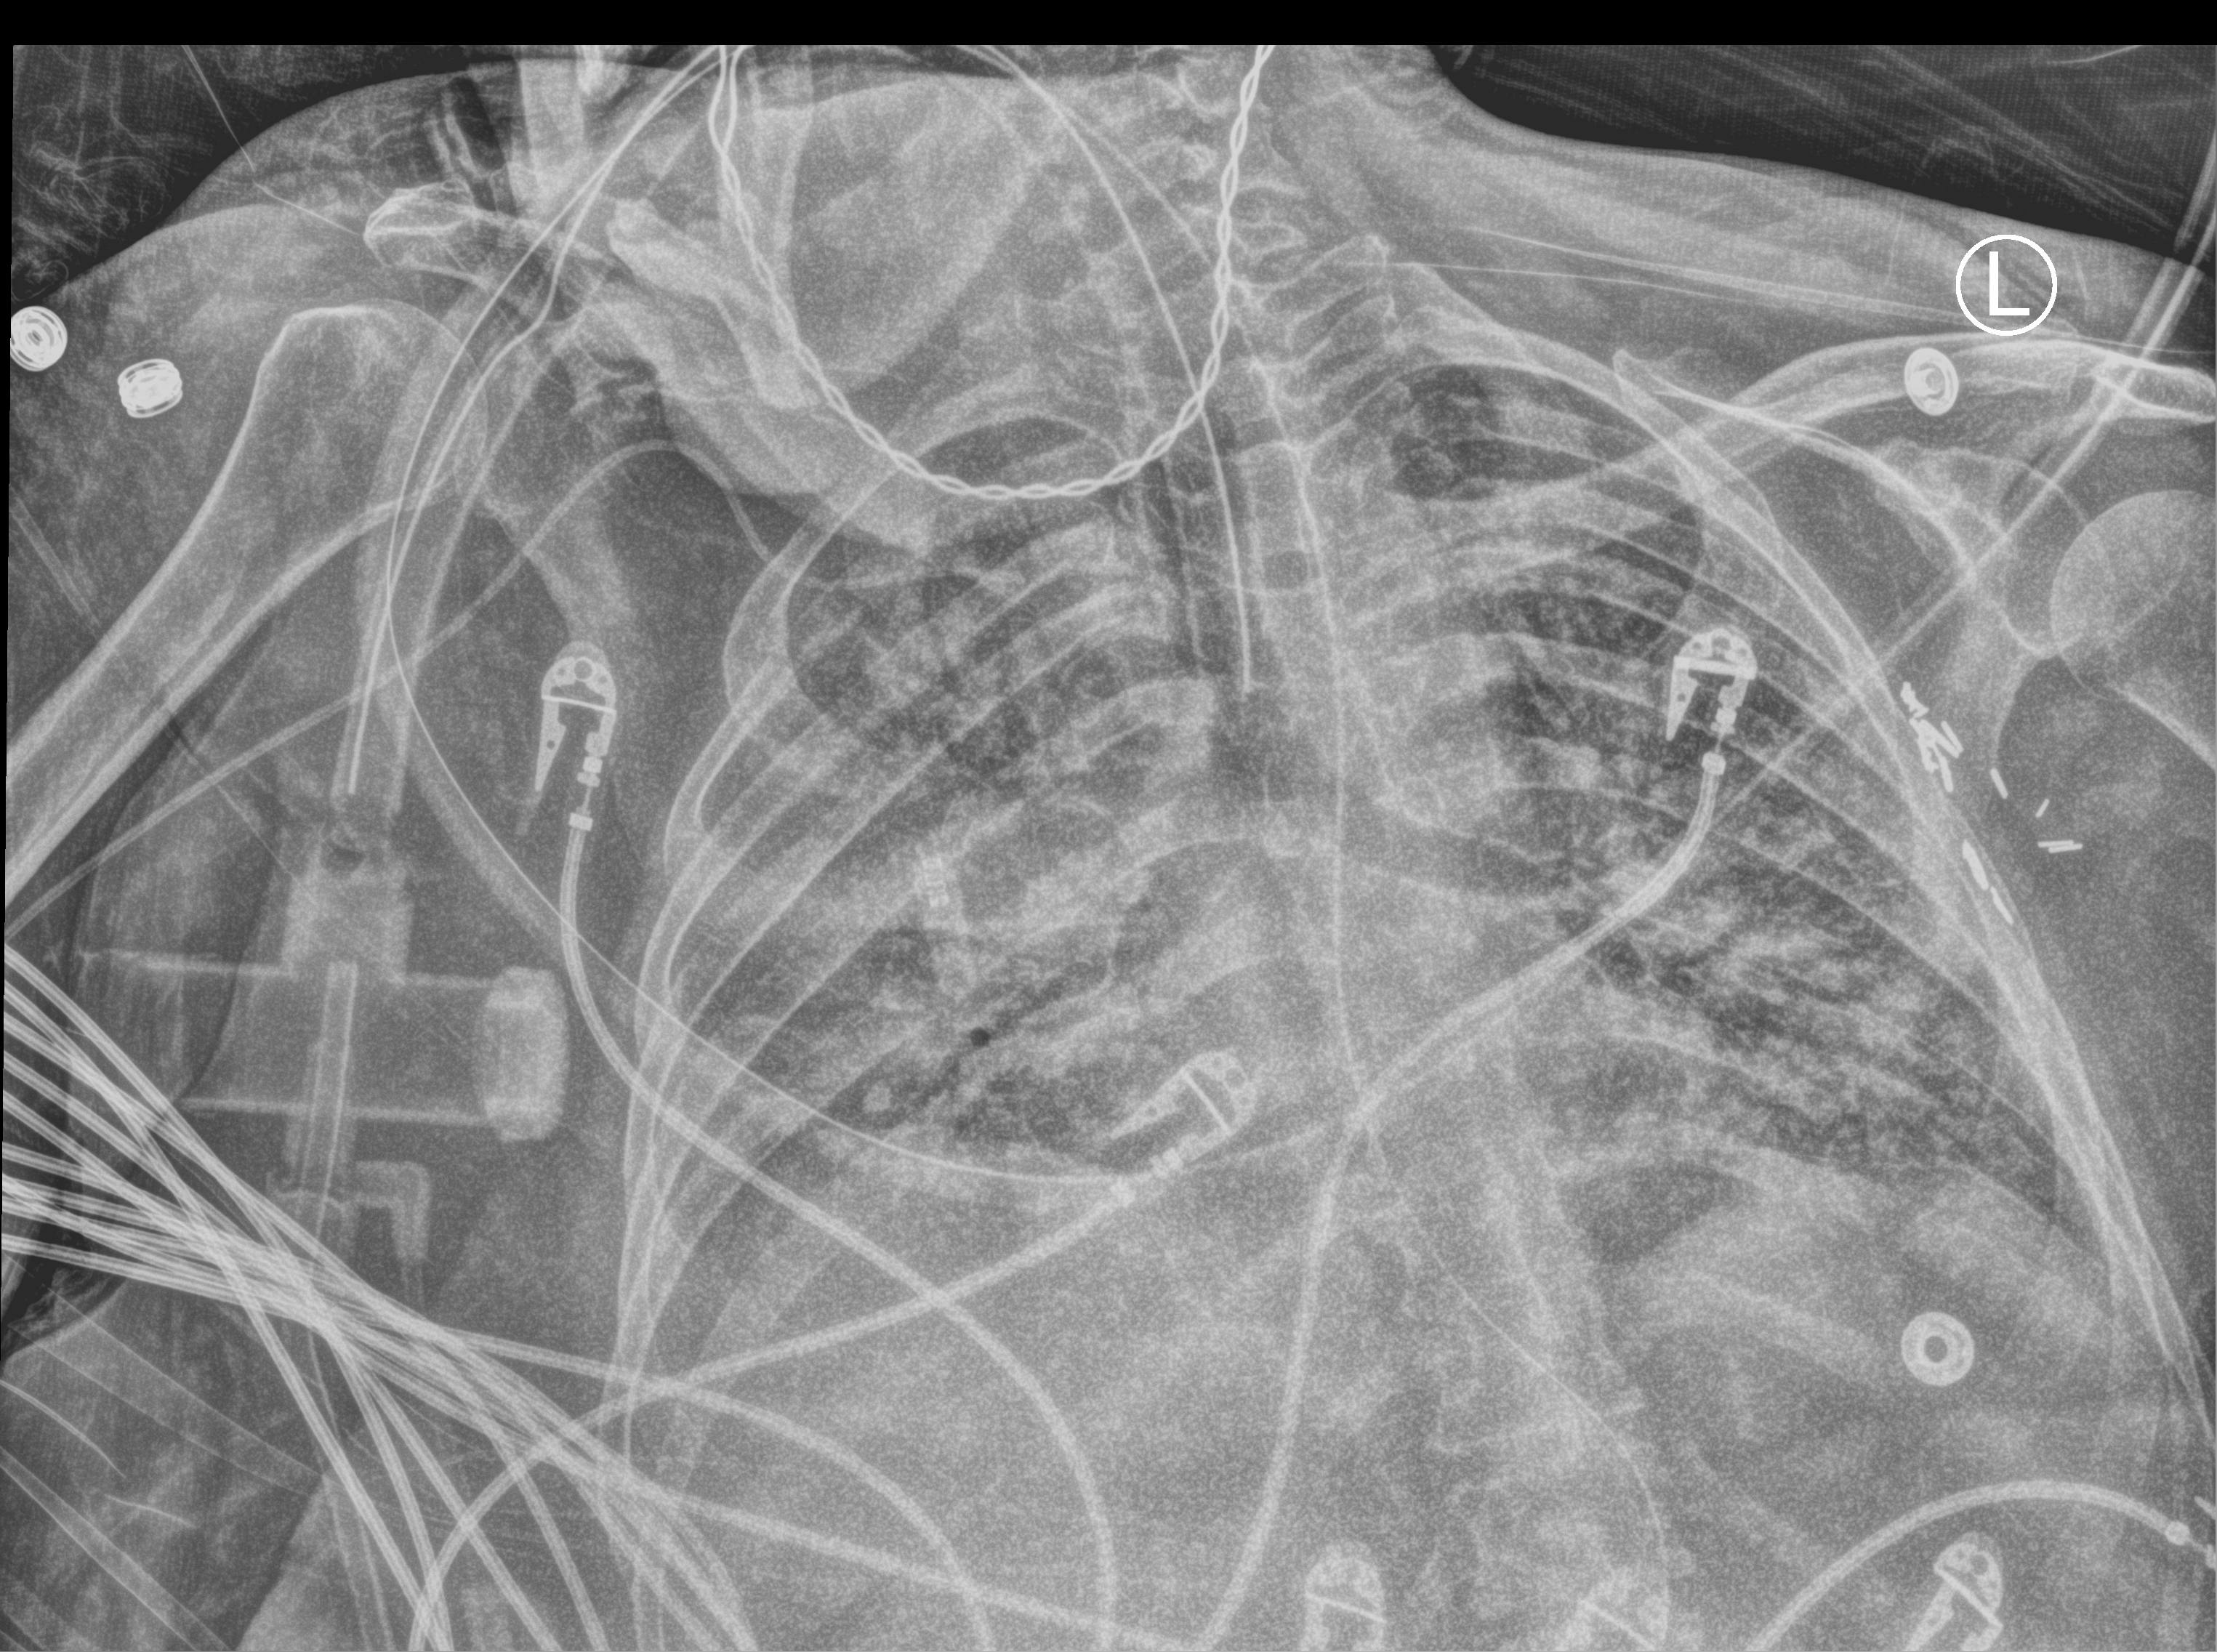
Bedside chest radiograph (computed radiography), anteroposterior (AP) projection. Female patient hospitalised with COVID-19, age 60–74 years.
Admission-level facts for this patient (not findings on this image; timing relative to this image not recorded): length of hospital stay: 16 days; mechanically ventilated during this hospital stay: yes.